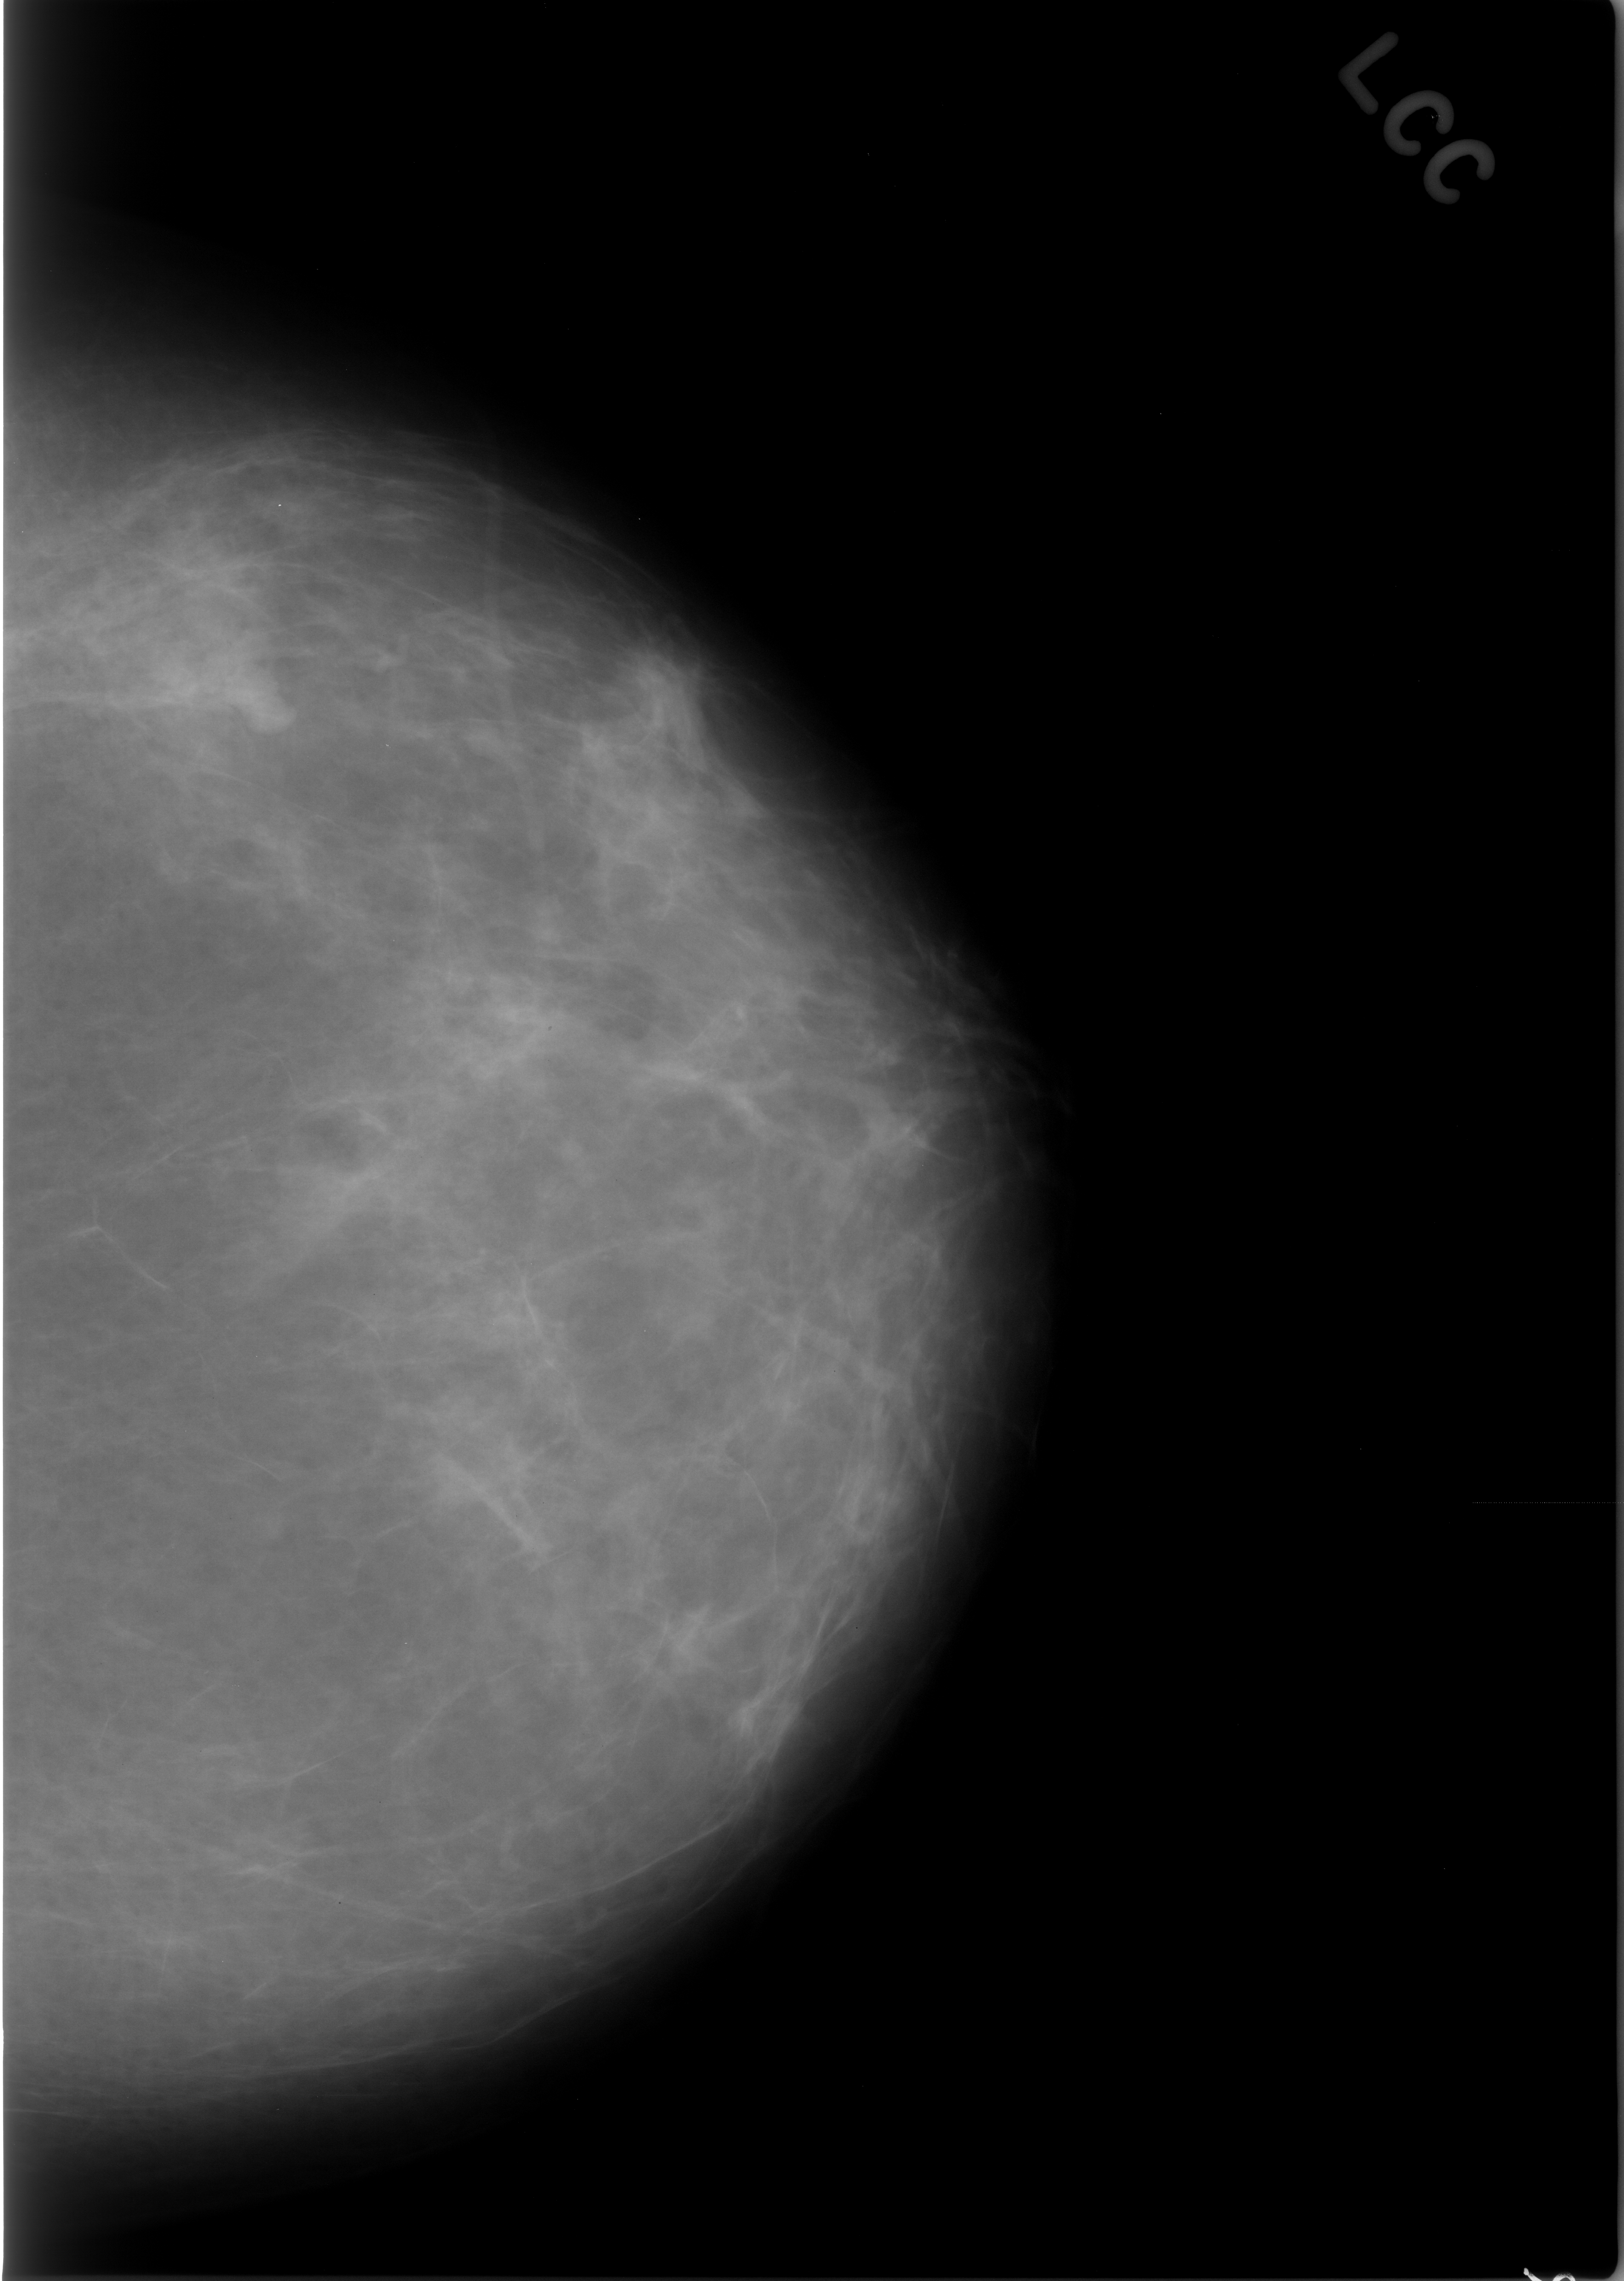
Scanned film-screen mammogram. Left breast. CC view. Breast composition: almost entirely fatty (BI-RADS density category 1 of 4). 1624 × 2281 image matrix.
Expert-marked regions of interest on this film, with their recorded descriptors:
- mass, shape irregular, margins spiculated; BI-RADS assessment category 4; subtlety rating 5 on a 1 (subtle) to 5 (obvious) scale; outcome (as recorded, no biopsy): benign without callback (not worked up further): bounding box [x1, y1, x2, y2] px = [589, 636, 716, 775]